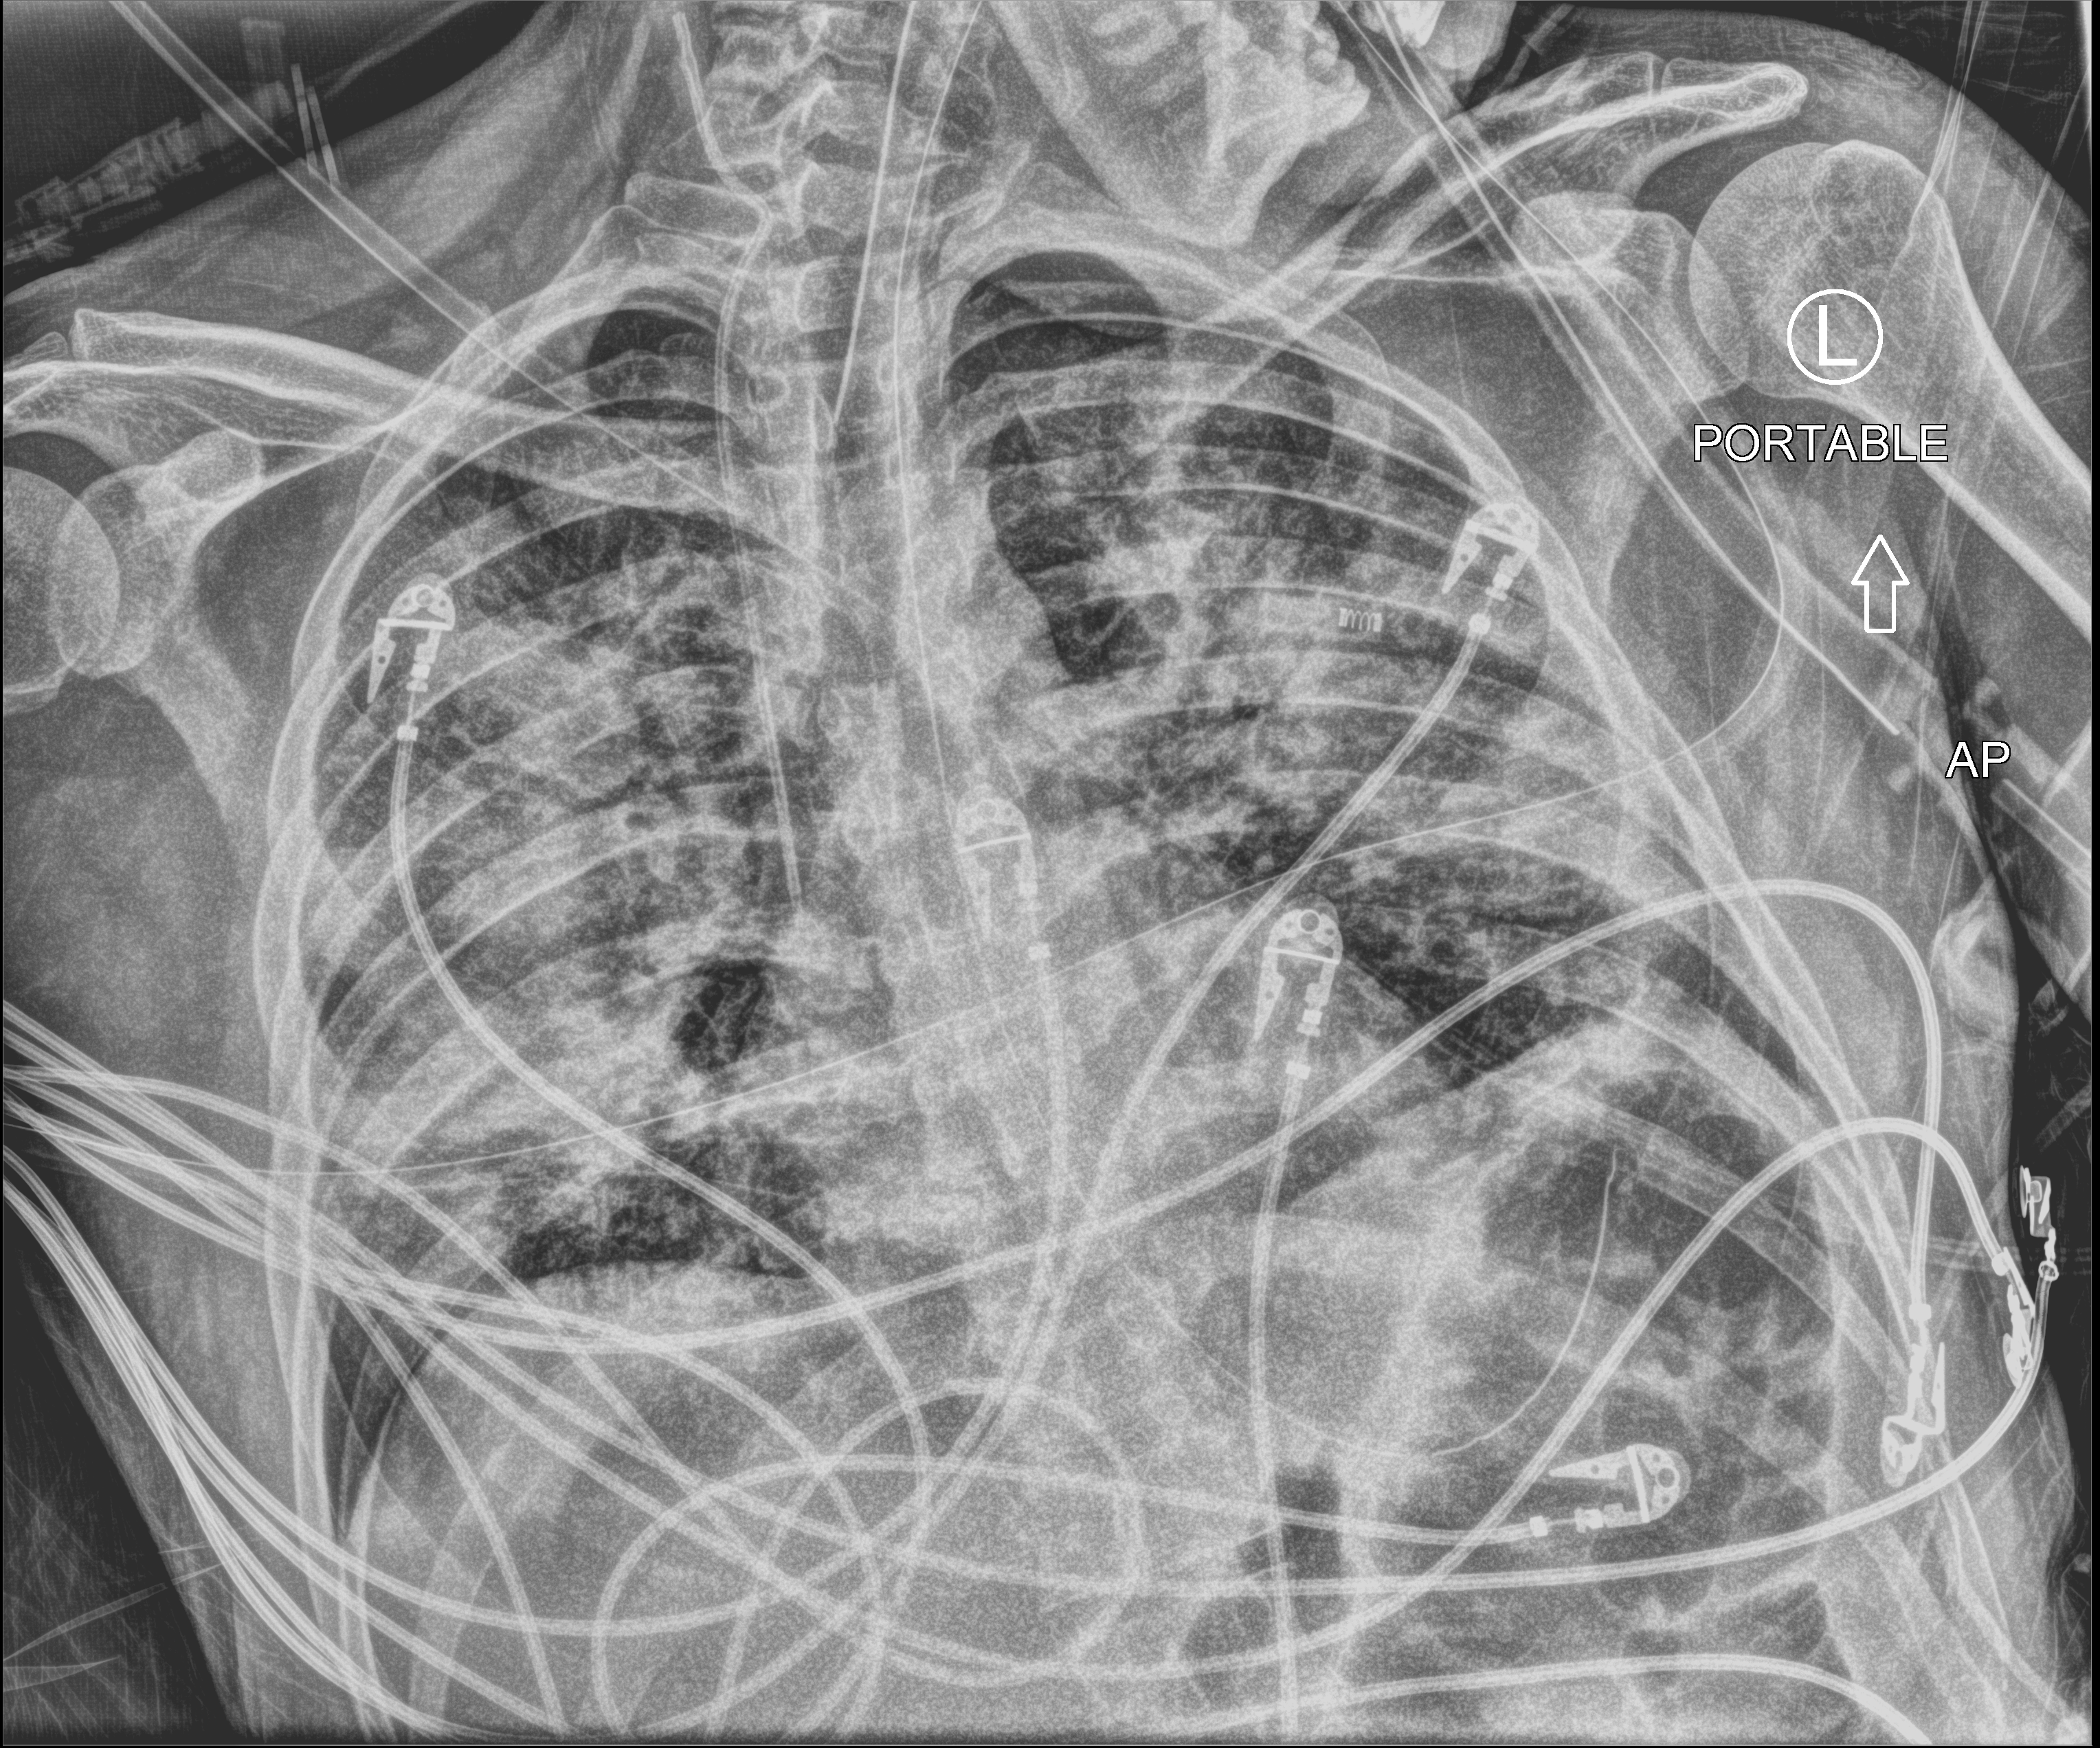
Chest X-ray (portable), anteroposterior (AP) projection. Patient hospitalised with COVID-19; male, aged 18–59 years.
Admission-level facts for this patient (not findings on this image; timing relative to this image not recorded): other chronic lung disease (admission record): no.